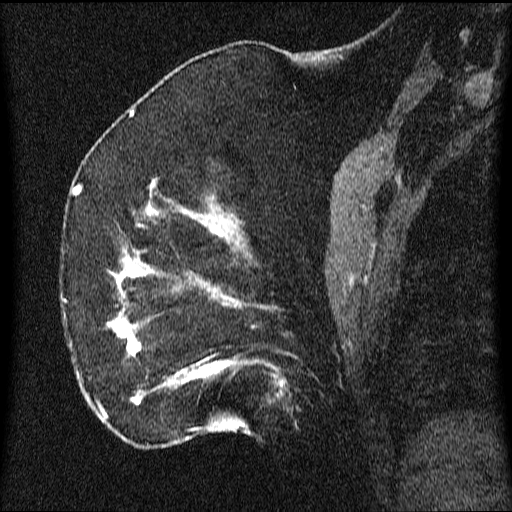
Breast MRI (dynamic contrast-enhanced), one sagittal slice. Position 21 of 64 along the scan axis. Dynamic contrast-enhanced series, image 2 of 3 at this slice position (ordered by acquisition). 1.5 T. TE 4.2 ms, TR 9.1 ms. 512 × 512 image matrix, field of view 180 × 180 mm. Patient: female, 52 years.
Outlined on this slice (semi-automatically segmented with operator editing):
- analysis volume of interest (the breast-tissue region the enhancement analysis was run in; not a lesion): bounding box (x1, y1, x2, y2) in pixels: (61, 203, 350, 438)
- tumour enhancement mask (voxels above the 70 % enhancement threshold inside the analysis volume of interest): (62, 208, 284, 432)